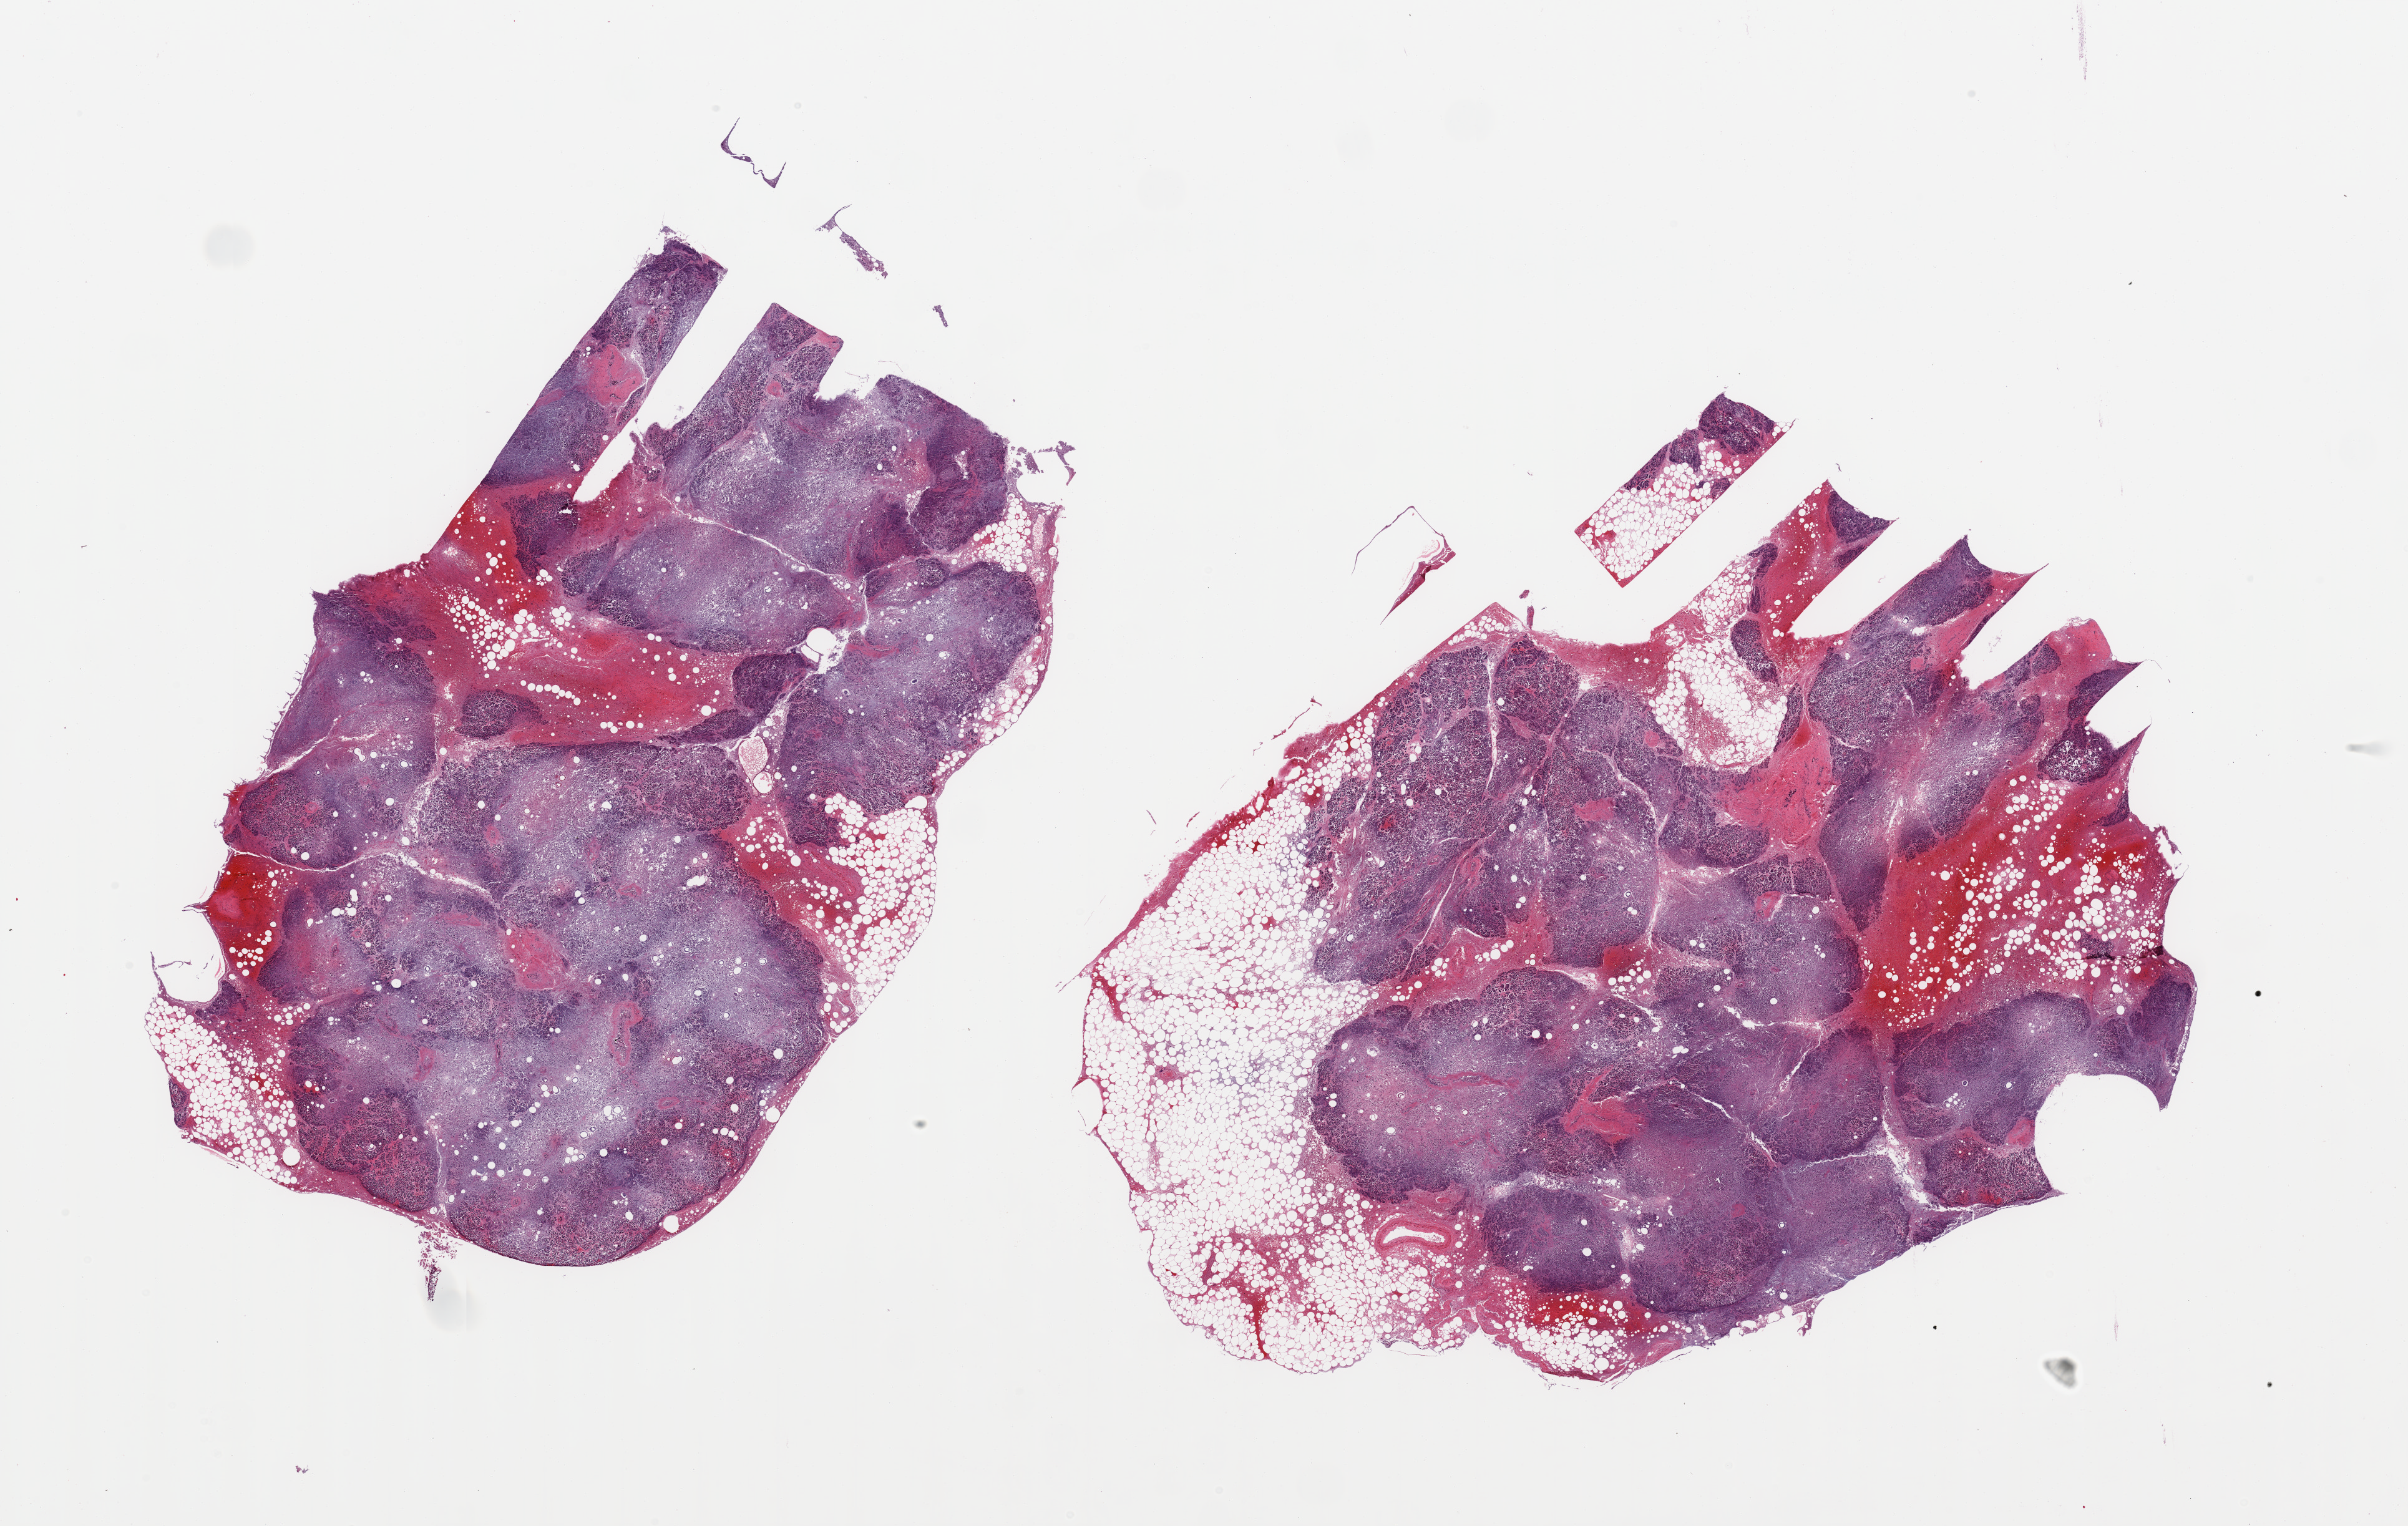
Digitized H&E-stained section, brightfield, whole scanned area (about 30.5 x 19.3 mm) shown as a low-resolution overview. PAXgene-fixed paraffin-embedded (PFPE) section. Sampled site (target tissue): pancreas. Donor tissue sample. Male donor.
Reviewer comment on this tissue sample: 2 pieces, advanced saponfication; islets completely degraded; ~20% adherent fat.